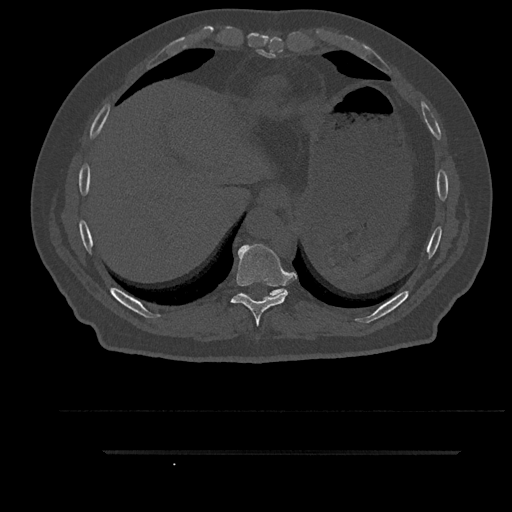
CT including the spine, one axial slice. Slice 415 of 797 in the series (ordered by position). Reconstruction kernel Br40s/3. 120 kVp. Bone window (W 1800 / L 400 HU). 0.5 mm slice thickness. 512 × 512 image matrix, field of view 432 × 432 mm. Patient: male, 63 years. From the clinical record (not read from this slice): primary cancer: renal; vertebrae with lytic lesions (as recorded): T8.
Annotated regions visible in this slice (semi-automatic segmentation, software-assisted and operator-edited):
- T10 vertebra: bounding box (x1, y1, x2, y2) in pixels: (239, 289, 286, 301)
- T9 vertebra: (231, 244, 291, 326)